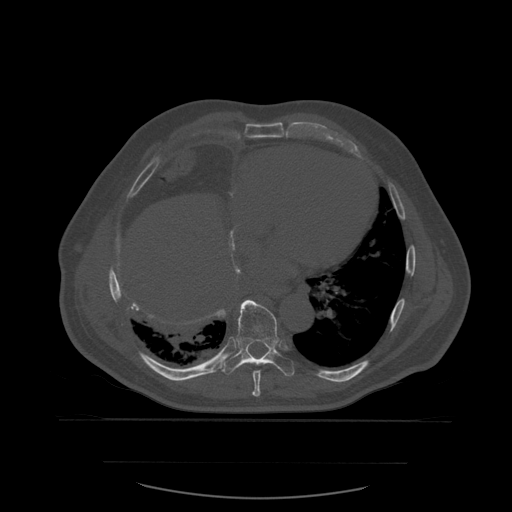
CT including the spine, one axial slice. Position 346 of 590 along the scan axis. Bone window (W 1800 / L 400 HU). 1.25 mm slice thickness. 512 × 512 image matrix. Patient age 71 years. Case-level facts recorded for this patient, not image findings: primary cancer: lung.
Outlined on this slice (semi-automatic segmentation, software-assisted and operator-edited):
- T8 vertebra: bounding box <252,371,261,397> (left, top, right, bottom; pixels)
- T9 vertebra: <220,300,295,377>